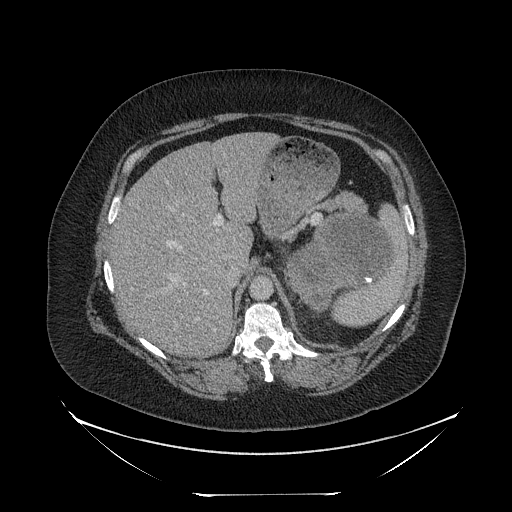
Contrast-enhanced abdominal CT, one axial slice. Position 162 of 205 along the scan axis. Reconstruction kernel STANDARD. Intravenous contrast given. Soft-tissue window (W 400 / L 40 HU). 512 × 512 image matrix, field of view 500 × 500 mm. Female patient, age 53 years. From the clinical record (not read from this slice): diagnosis: adrenocortical carcinoma; tumour side: left adrenal; tumour size at pathology: 17 cm; Ki-67 index: 20 %; stage (as recorded): 3.
Outlined on this slice (semi-automatically segmented with operator editing):
- mass: bounding box <289,216,389,307> (left, top, right, bottom; pixels)